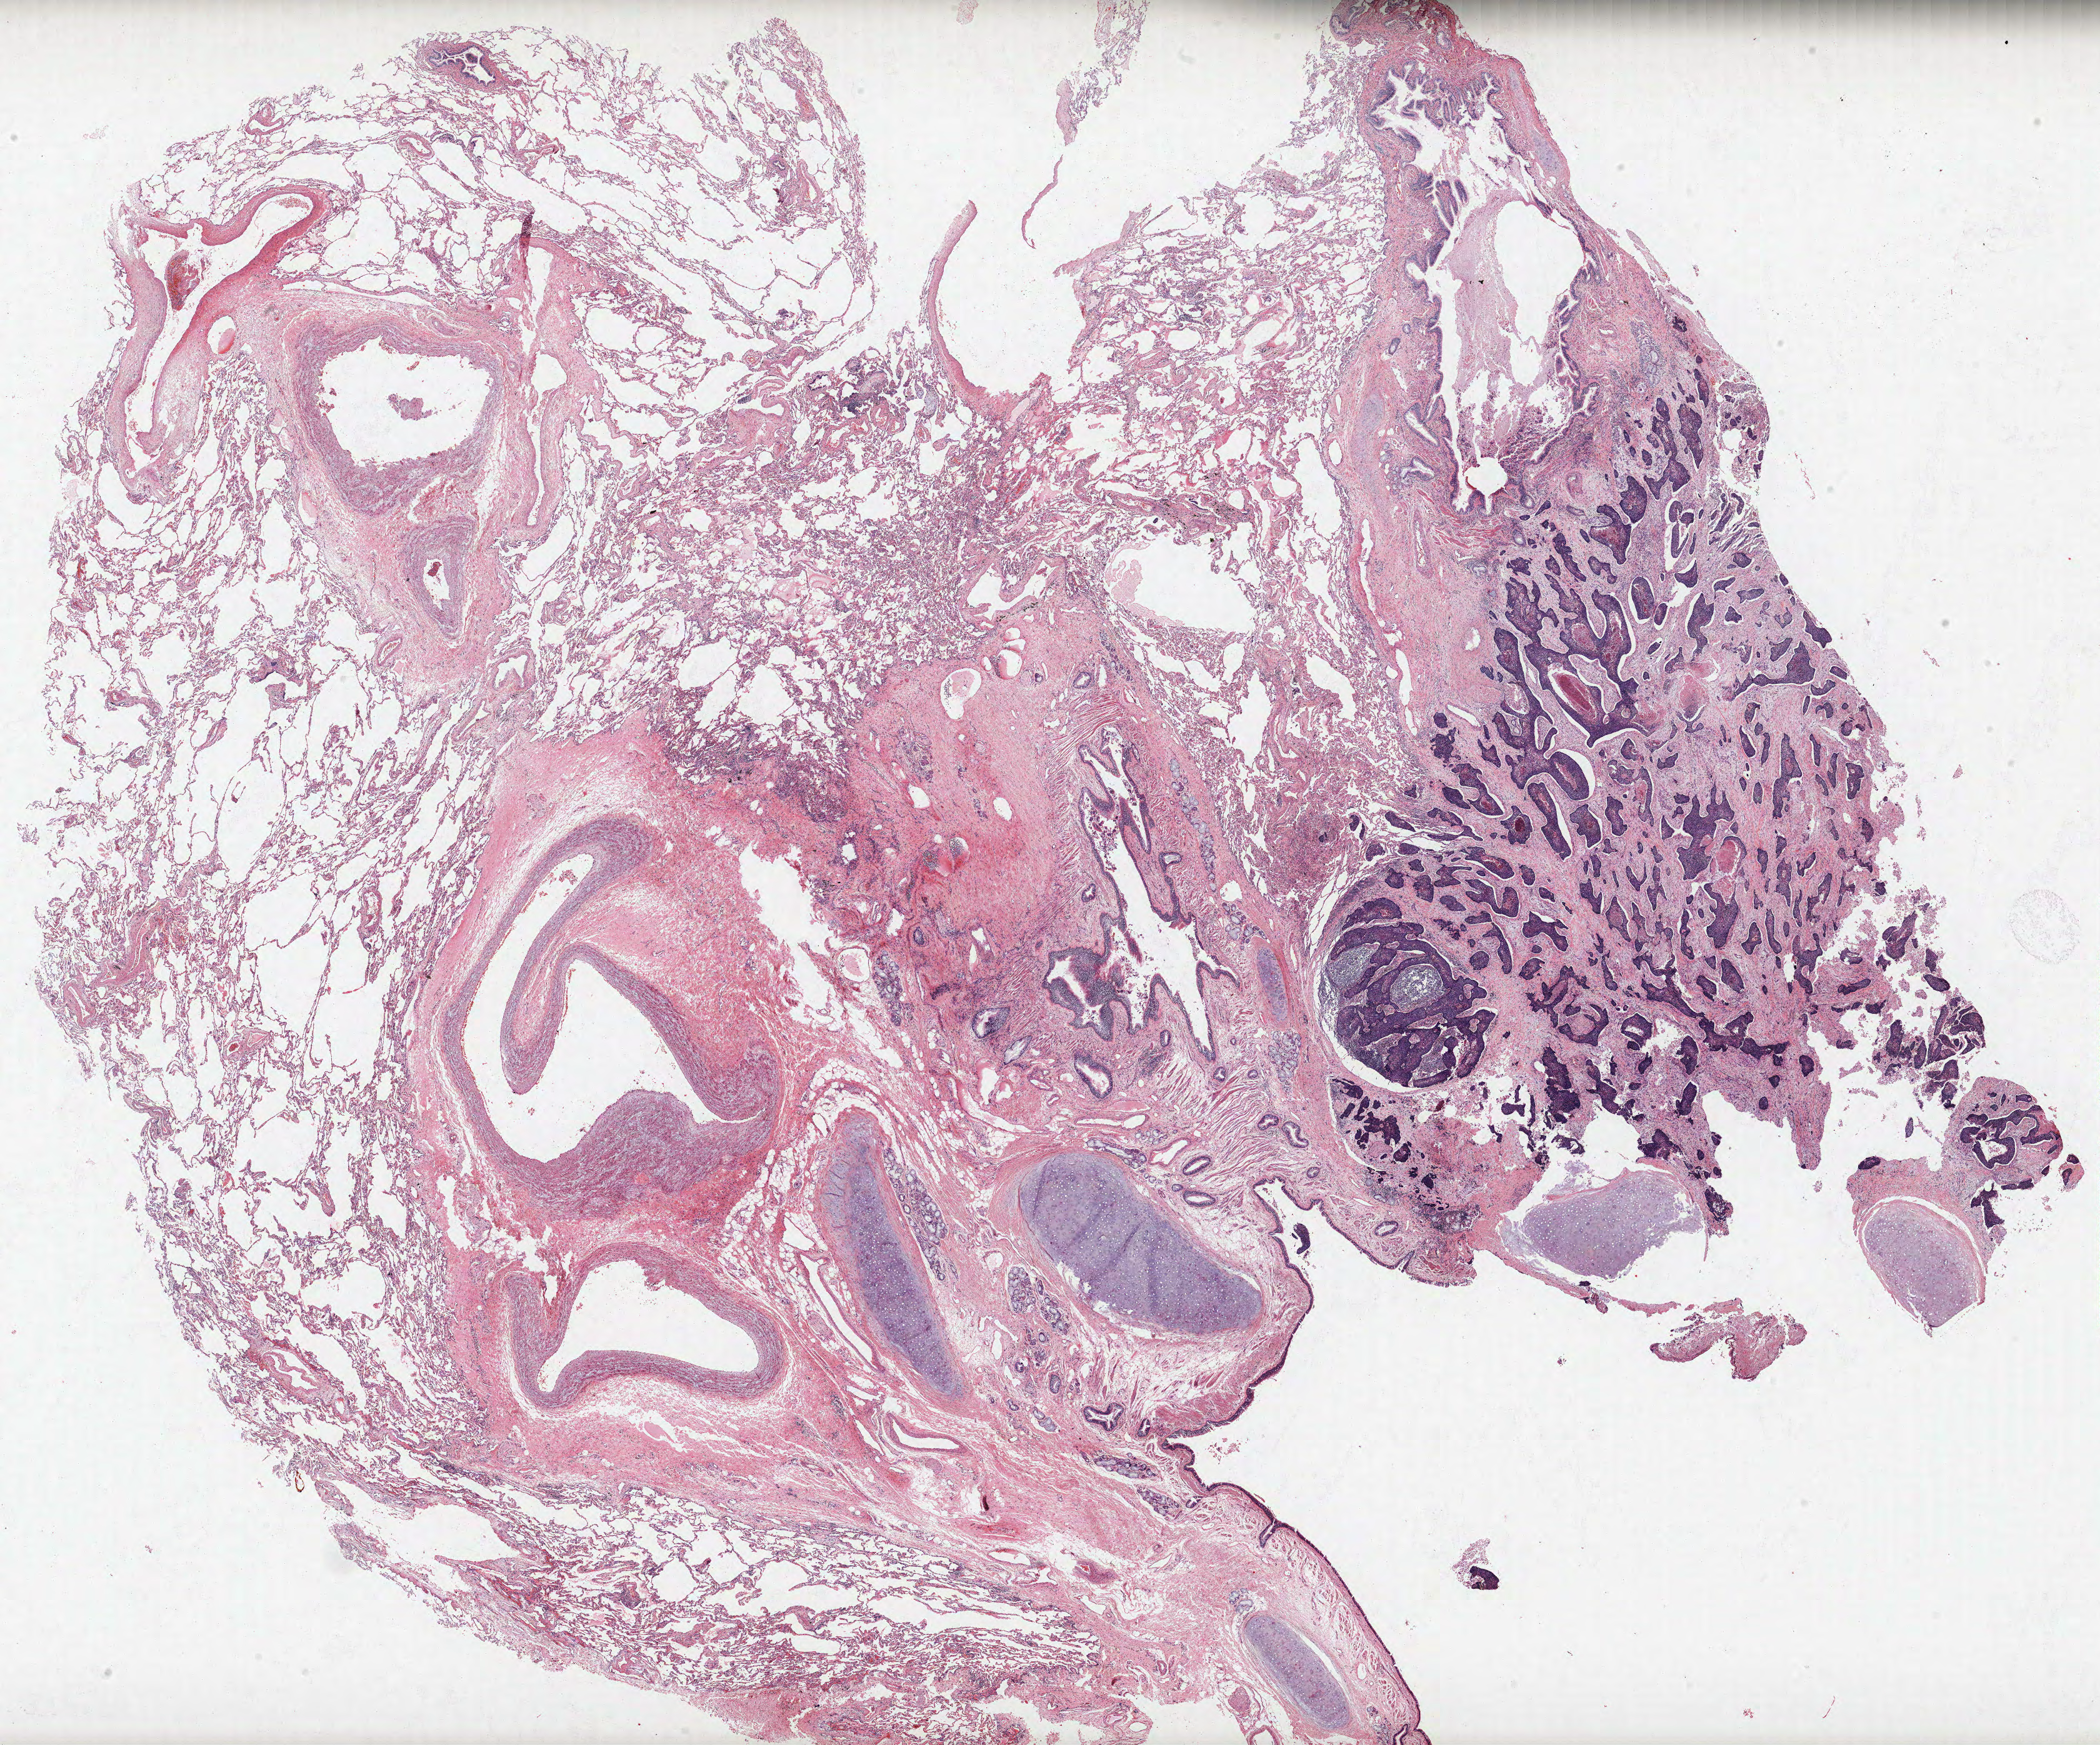
H&E-stained whole-slide image — a low-resolution overview of the entire scanned area, about 26.9 x 22.3 mm (from a 40x scan). FFPE section. Lung. Female, age 57 at enrolment. Grade: moderately differentiated (G2).
* stage (AJCC 6th edition): IIB
* participant's lung-cancer diagnosis: Basaloid squamous cell carcinoma
* tumour size (pathology): 32 mm
* primary tumour location (clinical record): left lower lobe